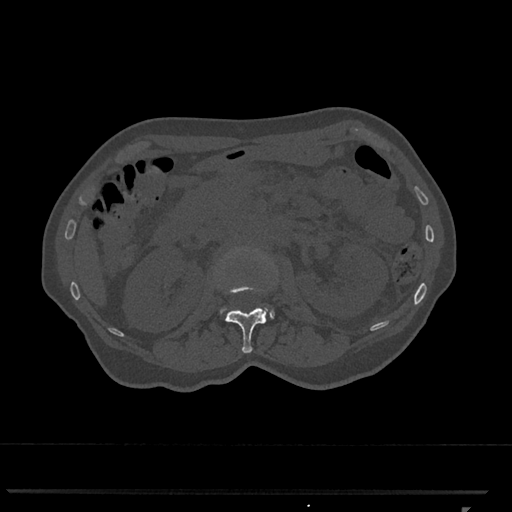
CT including the spine, one axial slice. Position 382 of 793 along the scan axis. Reconstruction kernel Br40s/3. Bone window (W 1800 / L 400 HU). 0.5 mm slice thickness. 512 × 512 image matrix. Patient: female, 62 years. From the clinical record (not read from this slice): primary cancer: renal.
Annotated regions visible in this slice (semi-automatically segmented with operator editing):
- L1 vertebra: bounding box [x1, y1, x2, y2] px = [218, 248, 268, 353]
- L2 vertebra: [221, 309, 275, 319]